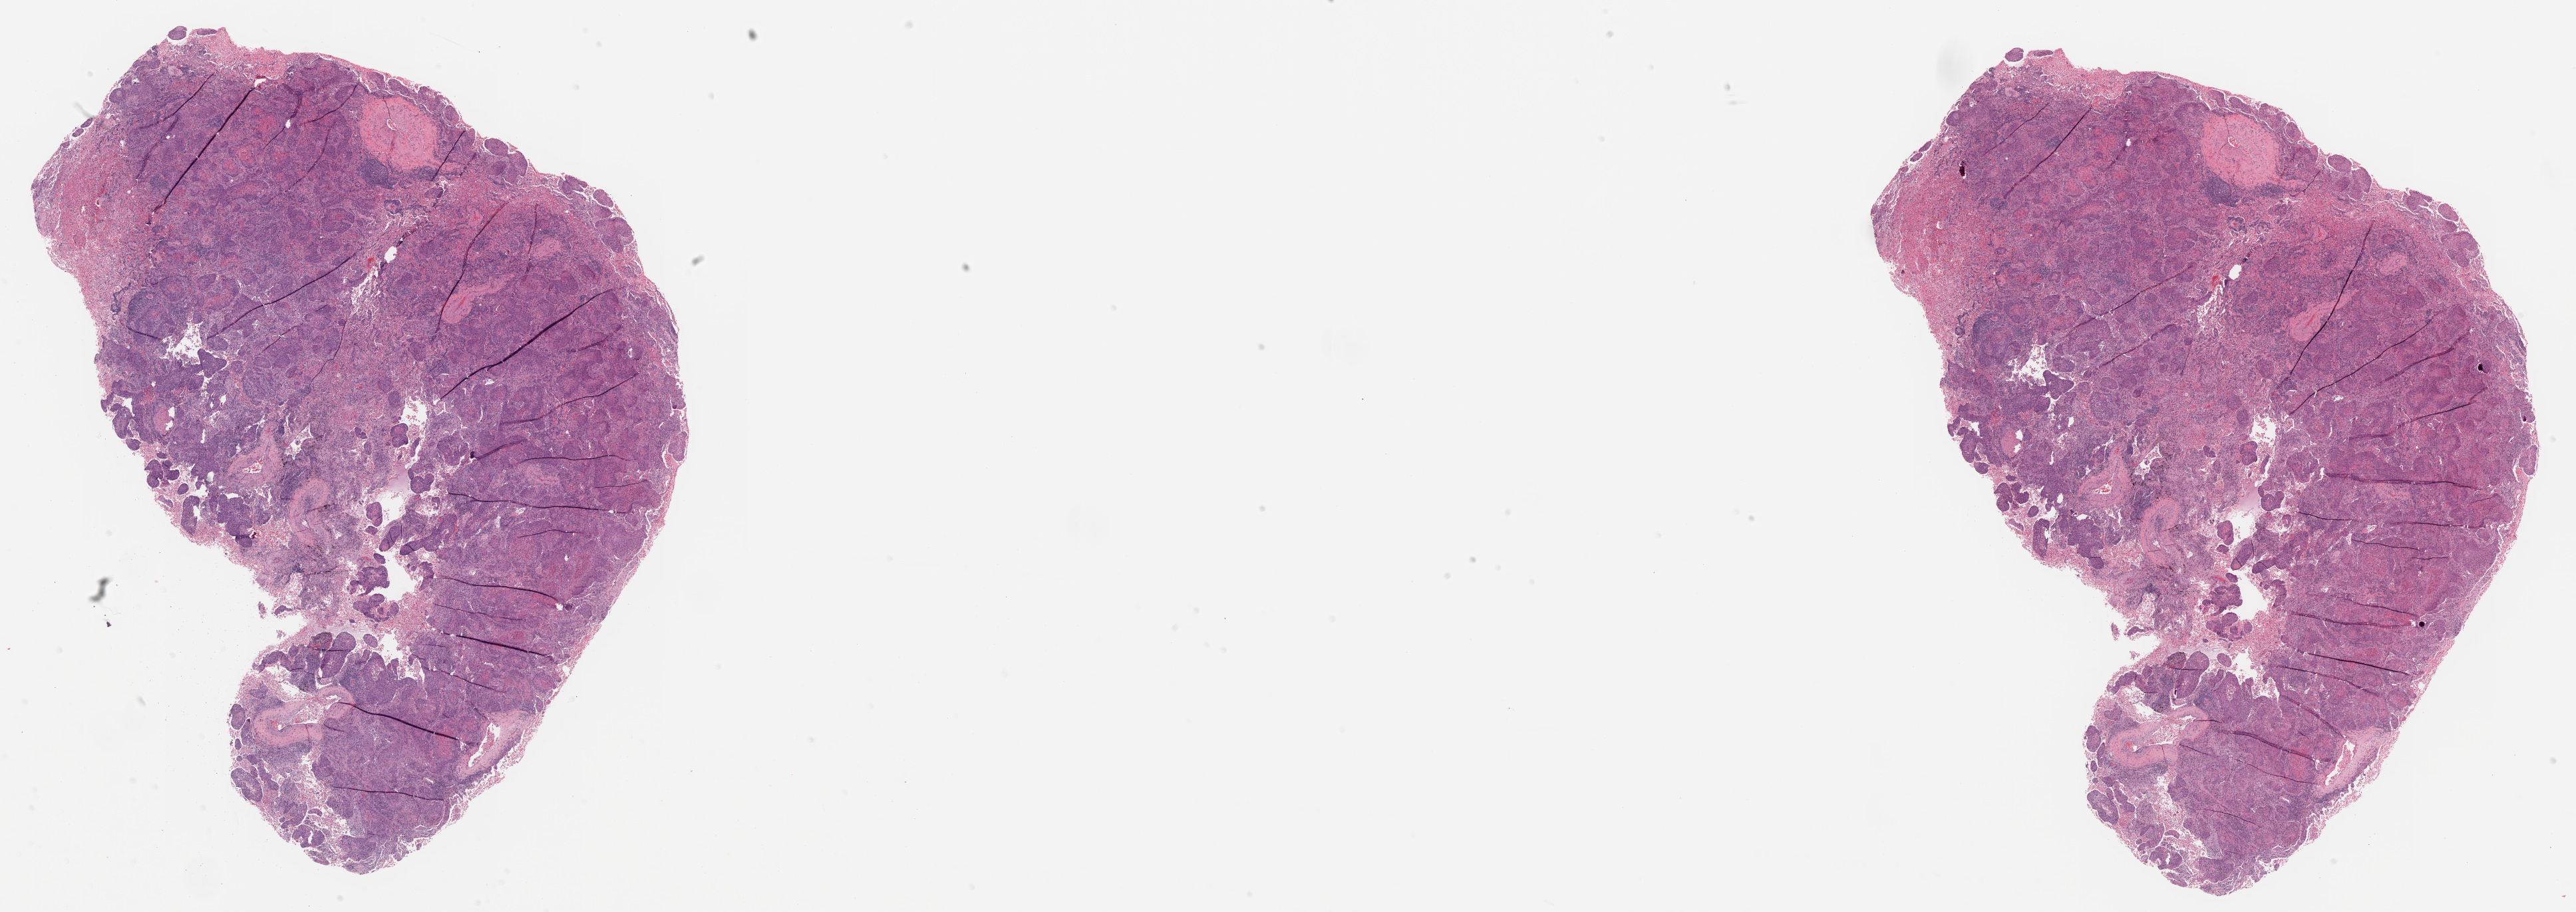
Whole-slide histology image, H&E — shown as a low-resolution overview of the whole scanned area (about 31.0 x 11.0 mm); formalin-fixed paraffin-embedded (FFPE) diagnostic section; primary tumour sample from the lung. Patient sex: male.
Histologic diagnosis: Squamous cell carcinoma, NOS (upper lobe, lung). AJCC pathologic stage: IA (6th edition). Laterality: left.